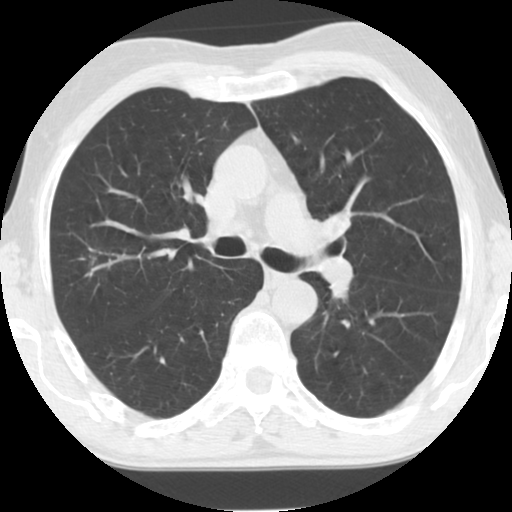
Low-dose screening chest CT, one axial slice; position 80 of 124 along the scan axis; reconstruction kernel STANDARD; 120 kVp; lung window (W 1500 / L -600 HU); 512 × 512 image matrix, field of view 310 × 310 mm.
Annotated regions visible in this slice (expert manual segmentation):
- lesion 1 (tumor, upper lobe of right lung): bounding box (x1, y1, x2, y2) in pixels: (92, 268, 100, 270)